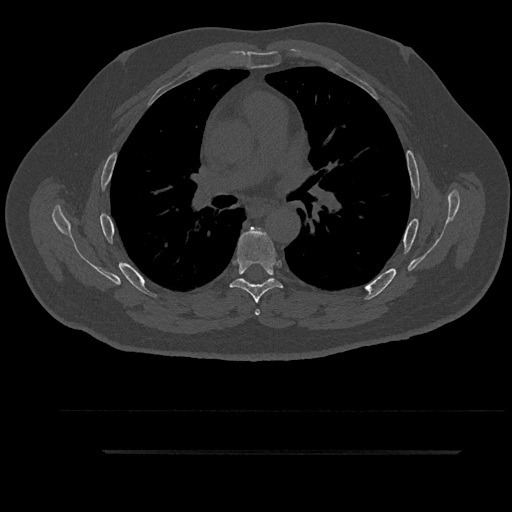
CT including the spine, one axial slice; slice 582 of 797 in the series (ordered by position); reconstruction kernel Br40s/3; 120 kVp; bone window (W 1800 / L 400 HU); 0.5 mm slice thickness; 512 × 512 image matrix. Male patient, age 63 years. Case-level facts recorded for this patient, not image findings: primary cancer: renal; vertebrae with lytic lesions (as recorded): T8.
Structures marked on this image (semi-automatic segmentation, software-assisted and operator-edited):
- T5 vertebra: bounding box [x1, y1, x2, y2] px = [244, 227, 266, 316]
- T6 vertebra: [230, 227, 283, 303]